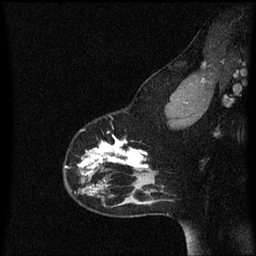
Breast MRI (dynamic contrast-enhanced), one sagittal slice; slice 46 of 60 in the series (ordered by position); dynamic contrast-enhanced series, image 2 of 3 at this slice position (ordered by acquisition); 1.5 T; TE 4.2 ms, TR 8.4 ms; 2 mm slice thickness; 256 × 256 image matrix, field of view 200 × 200 mm. Female patient, age 33 years.
Outlined on this slice (semi-automatic segmentation, software-assisted and operator-edited):
- analysis volume of interest (the breast-tissue region the enhancement analysis was run in; not a lesion): bounding box [x1, y1, x2, y2] px = [64, 116, 152, 191]
- tumour enhancement mask (voxels above the 70 % enhancement threshold inside the analysis volume of interest): [66, 132, 150, 189]